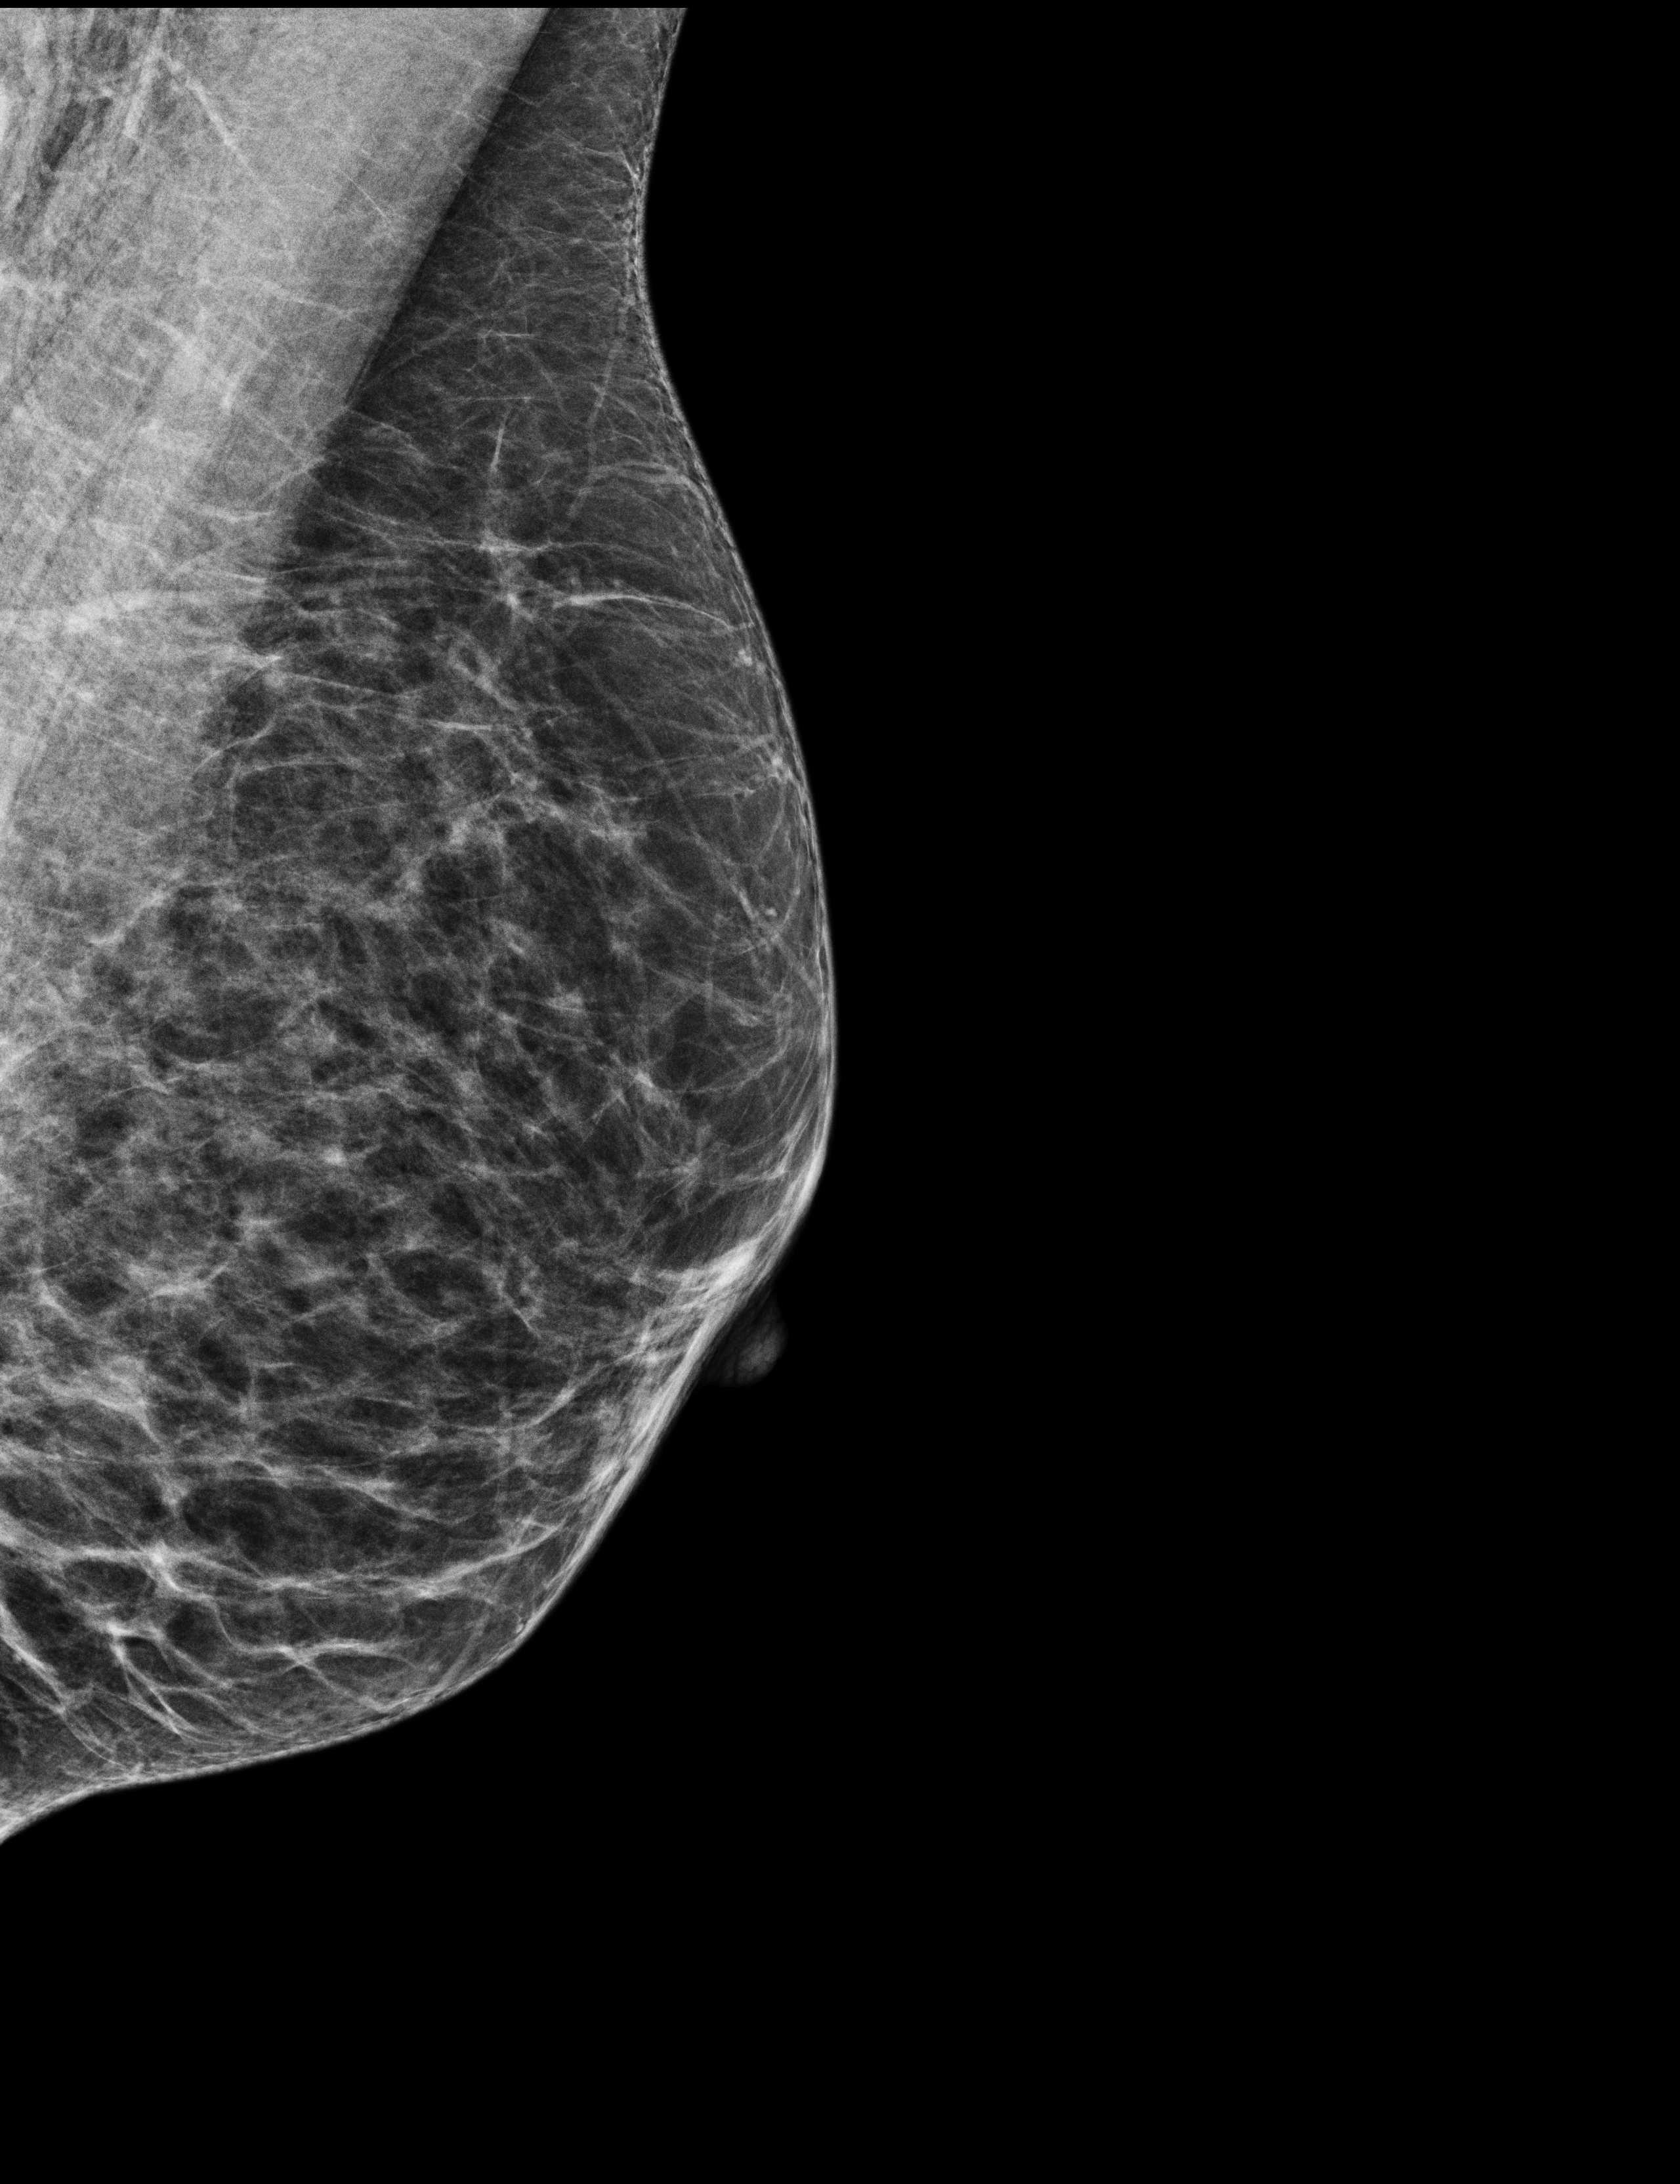
Screening examination, system: Selenia Dimensions. Patient aged 64 years (female).
Image type: full-field digital mammogram. Breast: left. Projection: medio-lateral oblique projection.